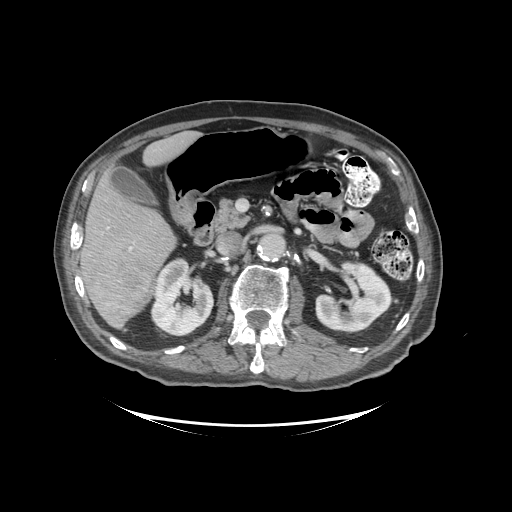
Contrast-enhanced abdominal CT (liver protocol), one axial slice; reconstruction kernel STANDARD; soft-tissue window (W 400 / L 40 HU); 2.5 mm slice thickness; 512 × 512 image matrix, field of view 460 × 460 mm. From the clinical record (not read from this slice): diagnosis: hepatocellular carcinoma (patient treated with transarterial chemoembolisation; whether this scan precedes or follows treatment is not stated here); TNM stage (as recorded): Stage-I; Child-Pugh class: A; tumour nodularity: uninodular.
Outlined on this slice (semi-automatic segmentation, software-assisted and operator-edited):
- liver parenchyma outside the tumour (the mass and vessels are separate outlines, so this box may not span the whole liver): bounding box [x1, y1, x2, y2] px = [80, 132, 197, 328]
- mass: [87, 260, 155, 319]
- liver vessels: [107, 228, 133, 251]